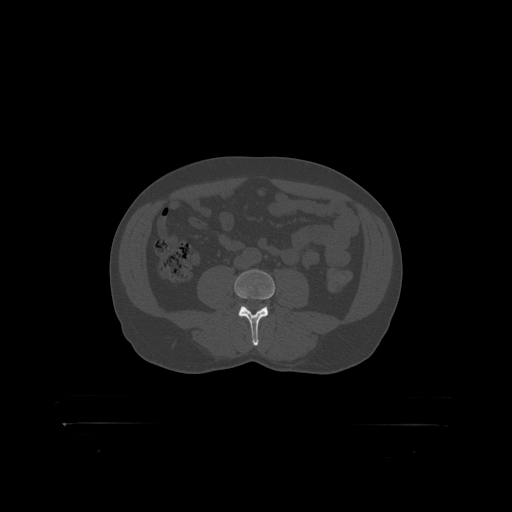
CT including the spine, one axial slice. Reconstruction kernel STANDARD. 120 kVp. Bone window (W 1800 / L 400 HU). 1.25 mm slice thickness. 512 × 512 image matrix, field of view 650 × 650 mm. Male patient, age 46 years. Case-level facts recorded for this patient, not image findings: primary cancer: skin.
Annotated regions visible in this slice (semi-automatic segmentation, software-assisted and operator-edited):
- L4 vertebra: box from (x=234, y=270) to (x=275, y=319) px